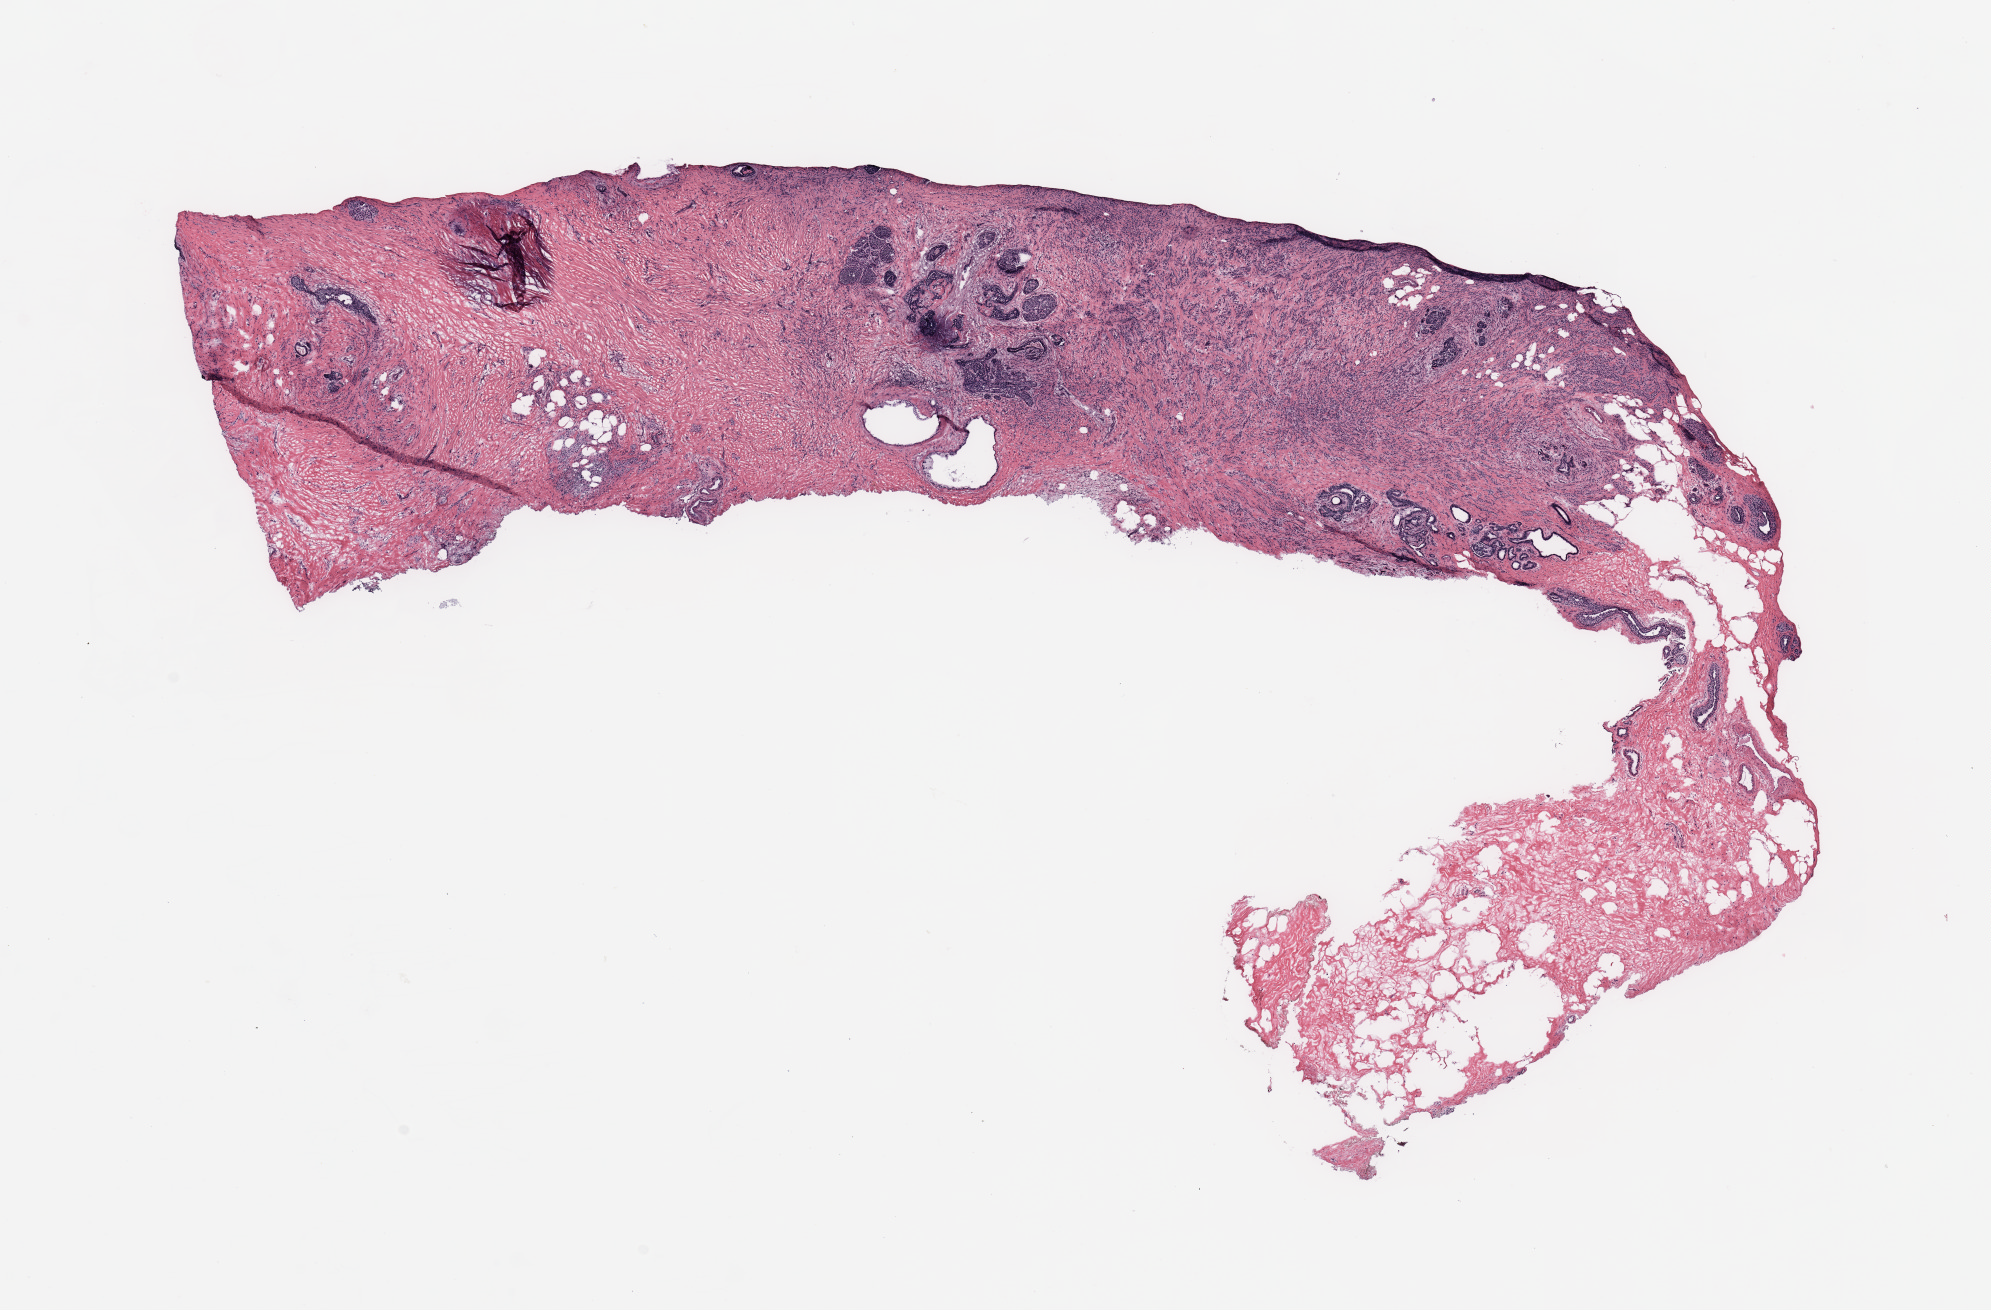
H&E whole-slide image — whole scanned area (about 15.8 x 10.4 mm, slide scanned at 20x) shown as a low-resolution overview, breast, tissue type not recorded.
• patient diagnosis (cohort enrolment): breast cancer (breast)